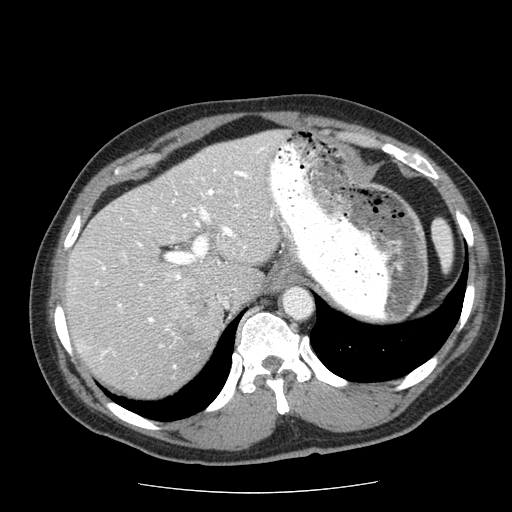
Contrast-enhanced abdominal CT (liver protocol), one axial slice; 120 kVp; soft-tissue window (W 400 / L 40 HU); 512 × 512 image matrix, field of view 360 × 360 mm. Case-level facts recorded for this patient, not image findings: diagnosis: hepatocellular carcinoma (patient treated with transarterial chemoembolisation; whether this scan precedes or follows treatment is not stated here); TNM stage (as recorded): Stage-IIIA; Child-Pugh class: A; tumour differentiation: well differentiated; tumour nodularity: multinodular.
Structures marked on this image (semi-automatic segmentation, software-assisted and operator-edited):
- liver parenchyma outside the tumour (the mass and vessels are separate outlines, so this box may not span the whole liver): bounding box [x1, y1, x2, y2] px = [64, 130, 286, 396]
- mass: [173, 290, 222, 369]
- liver vessels: [77, 147, 274, 368]